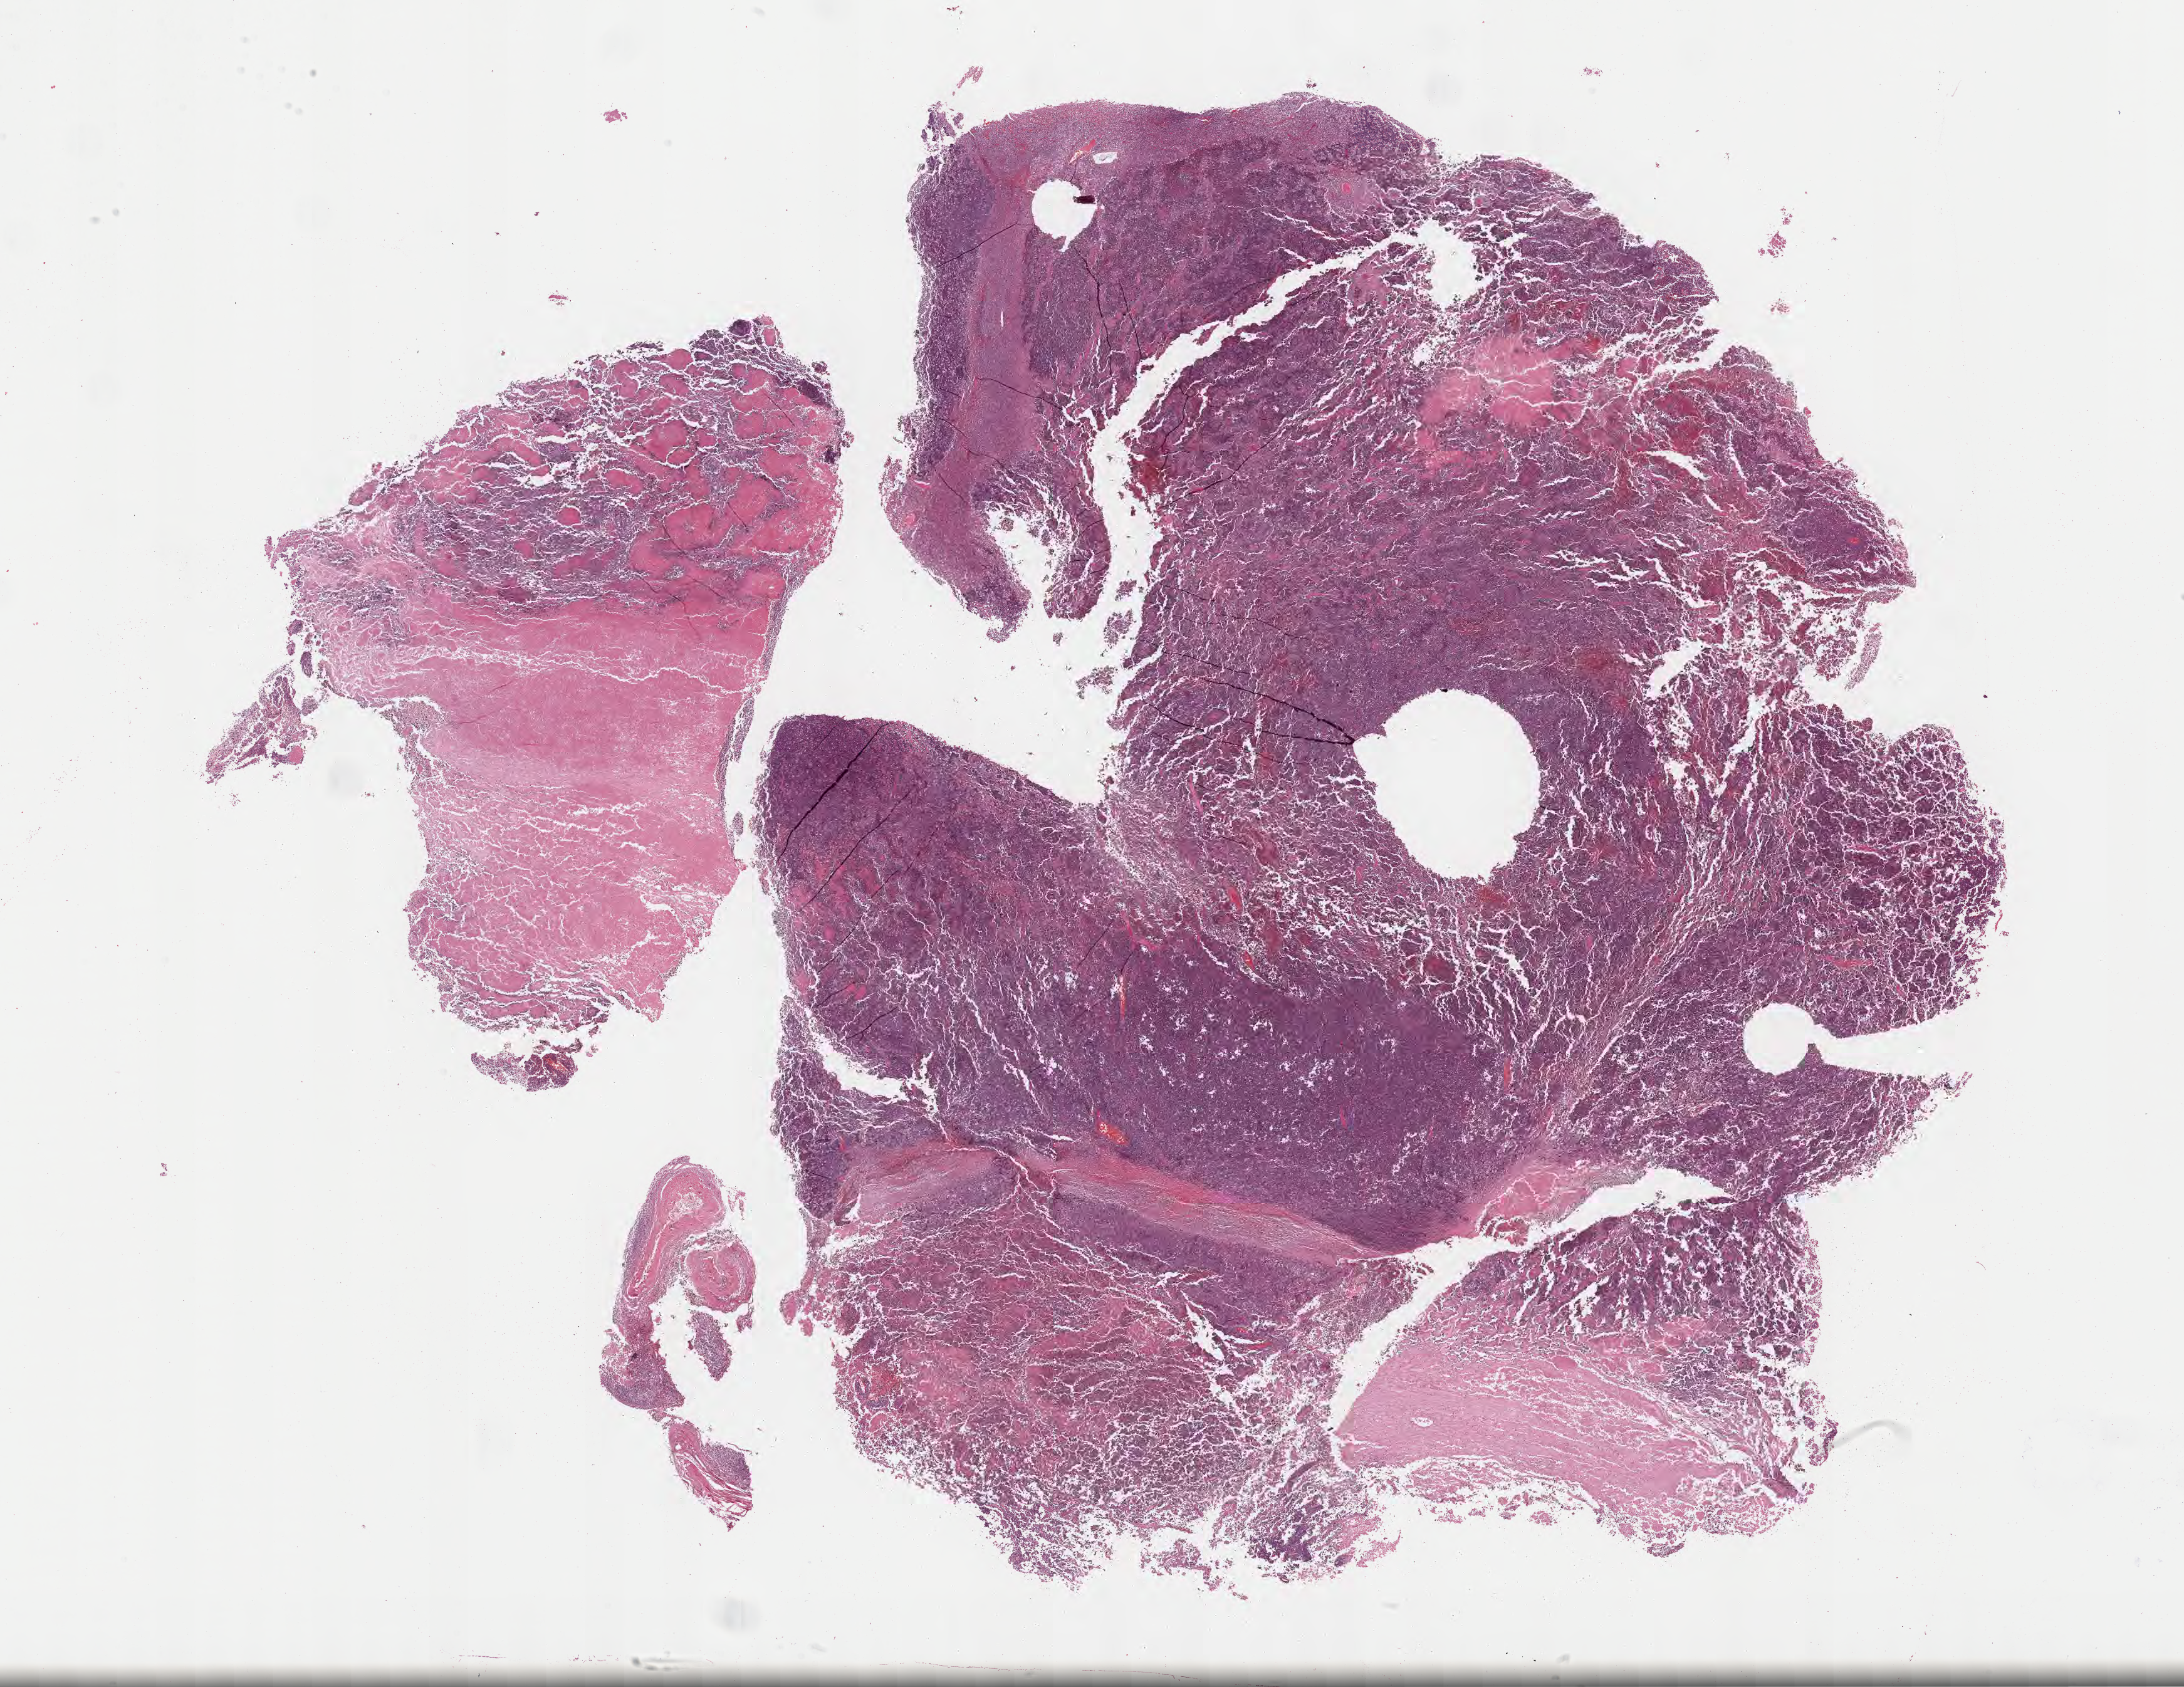
Digitized H&E-stained section, a low-resolution overview of the entire scanned area, about 28.2 x 21.8 mm; FFPE section; specimen: primary tumor. Patient: female, age 34 years.
Histologic diagnosis: Burkitt lymphoma, NOS.